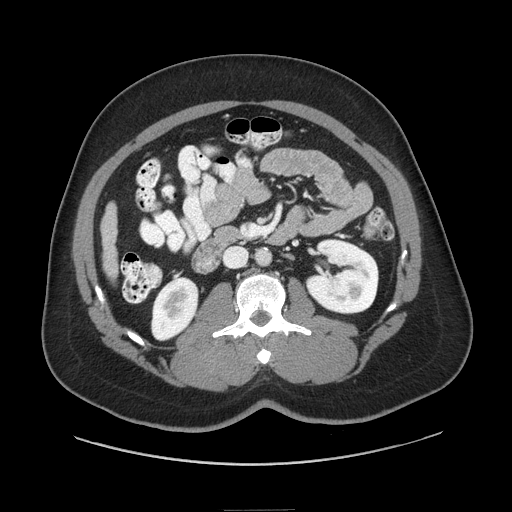
Contrast-enhanced abdominal CT (liver protocol), one axial slice. Position 17 of 87 along the scan axis. 140 kVp. Soft-tissue window (W 400 / L 40 HU). 512 × 512 image matrix, field of view 440 × 440 mm. From the clinical record (not read from this slice): diagnosis: hepatocellular carcinoma (patient treated with transarterial chemoembolisation; whether this scan precedes or follows treatment is not stated here); TNM stage (as recorded): Stage-II; Child-Pugh class: A; tumour differentiation: moderately differentiated; tumour nodularity: uninodular.
Outlined on this slice (semi-automatic segmentation, software-assisted and operator-edited):
- liver parenchyma outside the tumour (the mass and vessels are separate outlines, so this box may not span the whole liver): bounding box (x1, y1, x2, y2) in pixels: (100, 203, 117, 280)